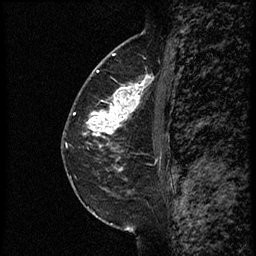
Breast MRI (dynamic contrast-enhanced), one sagittal slice; position 34 of 60 along the scan axis; dynamic contrast-enhanced study with each time point stored as its own series, time point 2 of 3 at this slice position (early post-contrast, ordered by acquisition time); 1.5 T; TE 4.2 ms, TR 18.9 ms; 2 mm slice thickness; 256 × 256 image matrix, field of view 200 × 200 mm. Female patient. Case-level facts recorded for this patient, not image findings: setting: breast cancer imaged before/during neoadjuvant chemotherapy; receptor status: HER2-positive.
Annotated regions visible in this slice (semi-automatically segmented with operator editing):
- analysis volume of interest (the breast-tissue region the enhancement analysis was run in; not a lesion): bounding box <89,67,161,147> (left, top, right, bottom; pixels)
- tumour enhancement mask (voxels above the 100 % enhancement threshold inside the analysis volume of interest): <90,76,152,147>